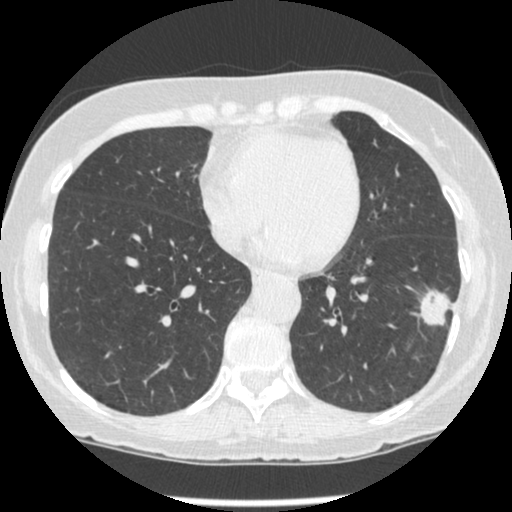
Low-dose screening chest CT, one axial slice; slice 92 of 247 in the series (ordered by position); reconstruction kernel STANDARD; 120 kVp; lung window (W 1500 / L -600 HU); 1.25 mm slice thickness; 512 × 512 image matrix, field of view 303 × 303 mm.
Annotated regions visible in this slice (expert manual segmentation):
- lesion 1 (tumor, lower lobe of left lung): bounding box <419,290,452,326> (left, top, right, bottom; pixels)